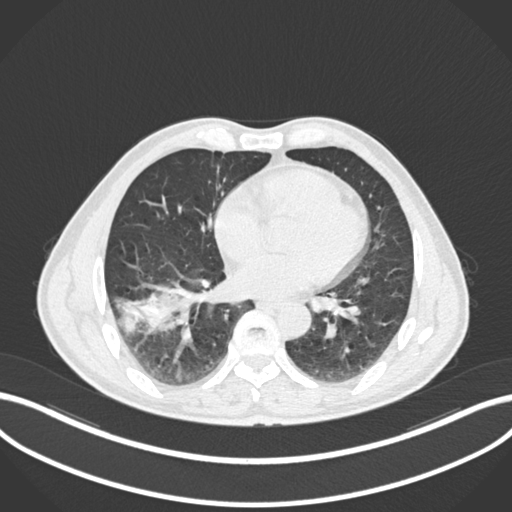
Chest CT, one axial slice; slice 74 of 208 in the series (ordered by position); reconstruction kernel B30f; 120 kVp; lung window (W 1500 / L -600 HU); 1 mm slice thickness; 512 × 512 image matrix, field of view 400 × 400 mm. Male patient, age 58 years. Case-level facts recorded for this patient, not image findings: clinical TNM (as recorded): T3 N0 M0.
Structures marked on this image (rectangle marked by the reading radiologist):
- lung tumour (recorded histology: squamous cell carcinoma): box from (x=117, y=278) to (x=194, y=341) px